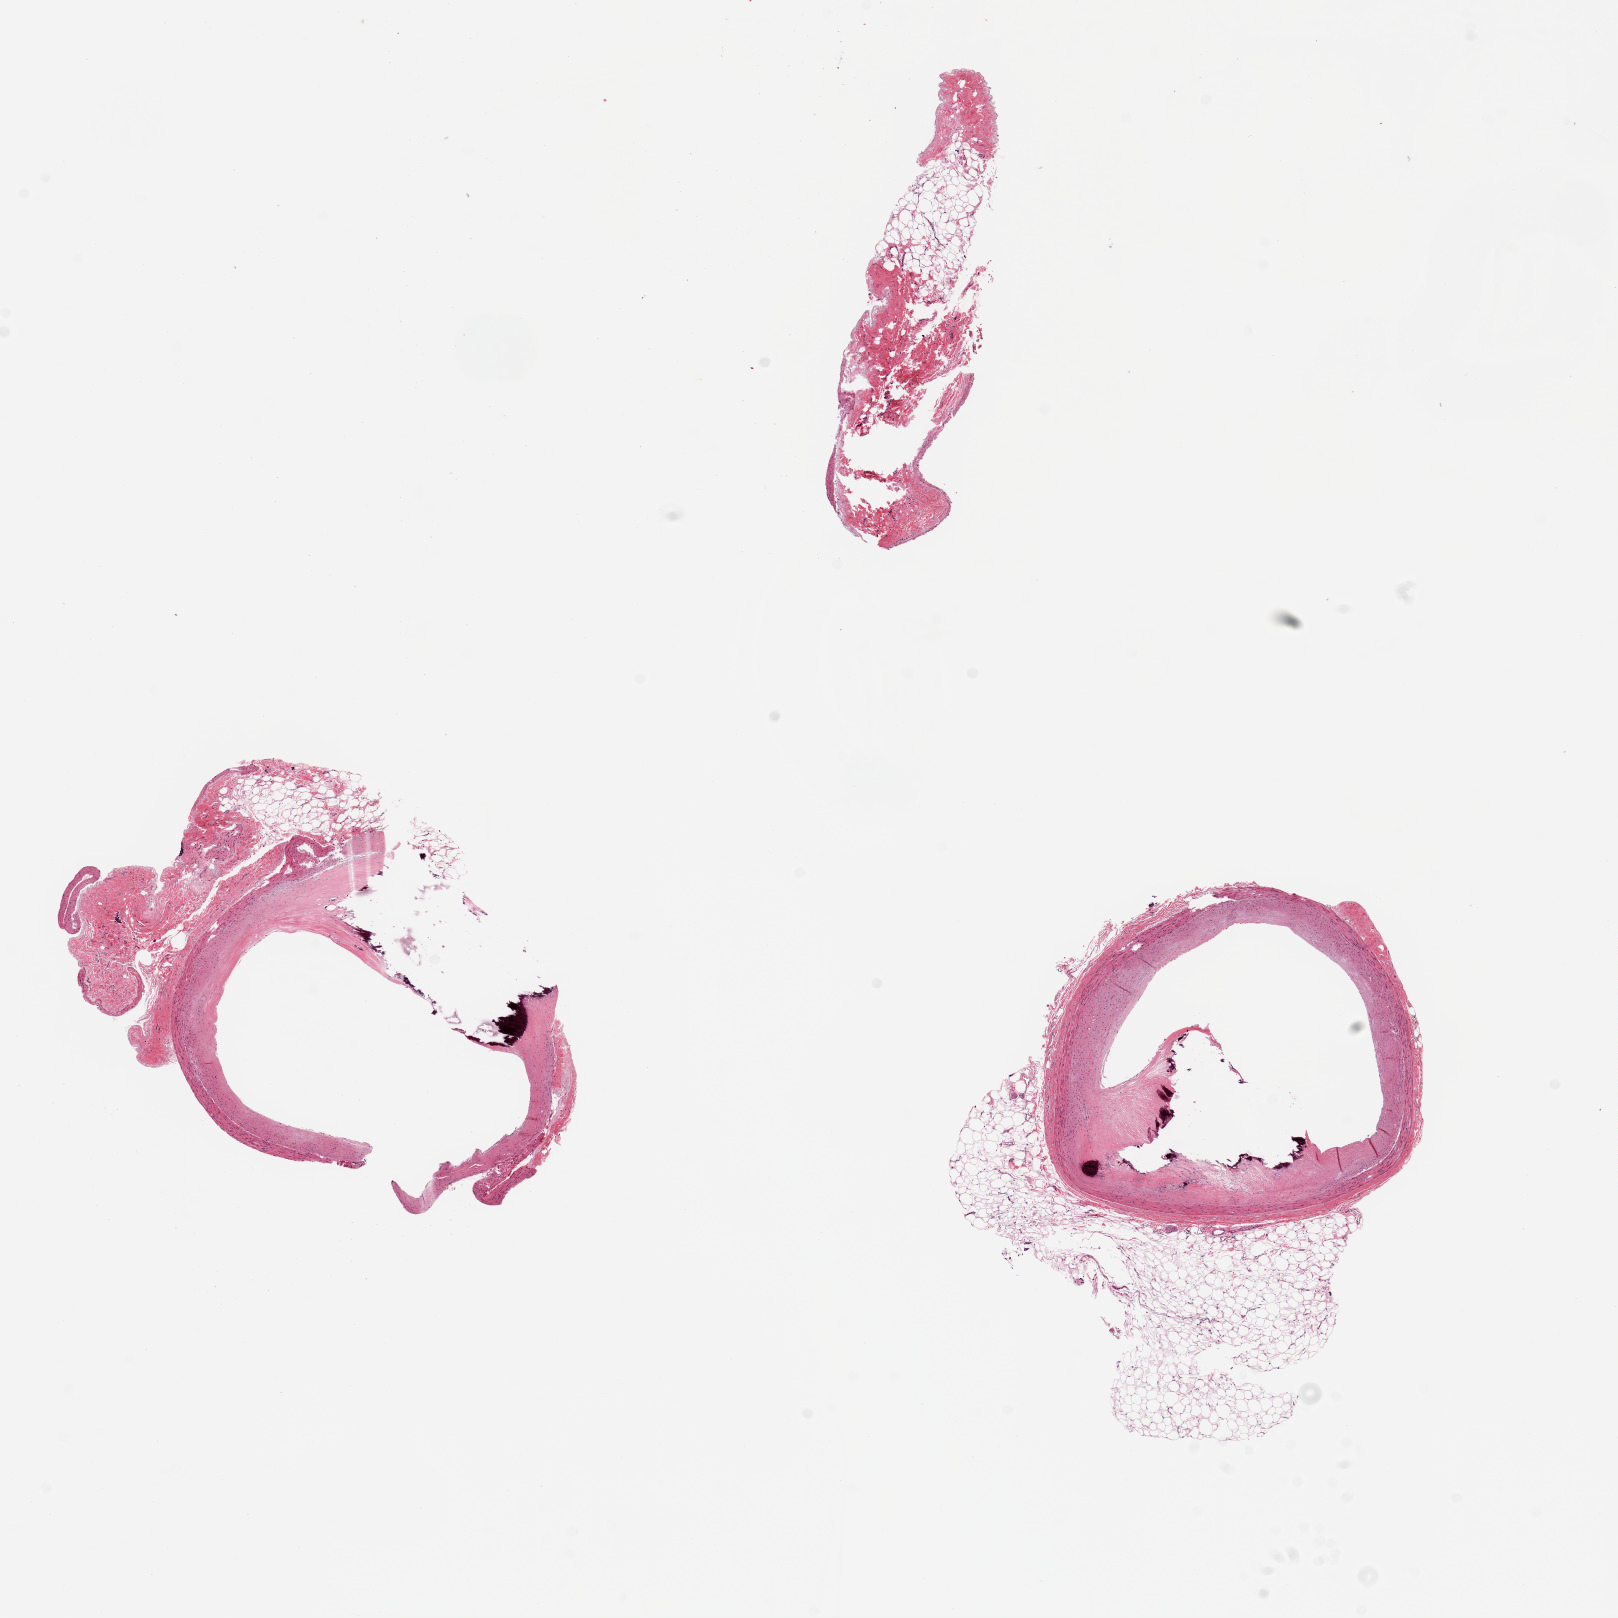
Haematoxylin and eosin whole-slide image, whole scanned area (about 12.8 x 12.8 mm, from a 20x scan) shown as a low-resolution overview; PAXgene-fixed paraffin-embedded (PFPE) section; sampled site (target tissue): coronary artery; donor tissue sample. Male donor.
• reviewer comment on this tissue sample: 2 ~ 2x2.5mm pieces. Calcified atherosclerosis causes ~35% luminal occlusion. 2mm nubbins of fat on both aliquots